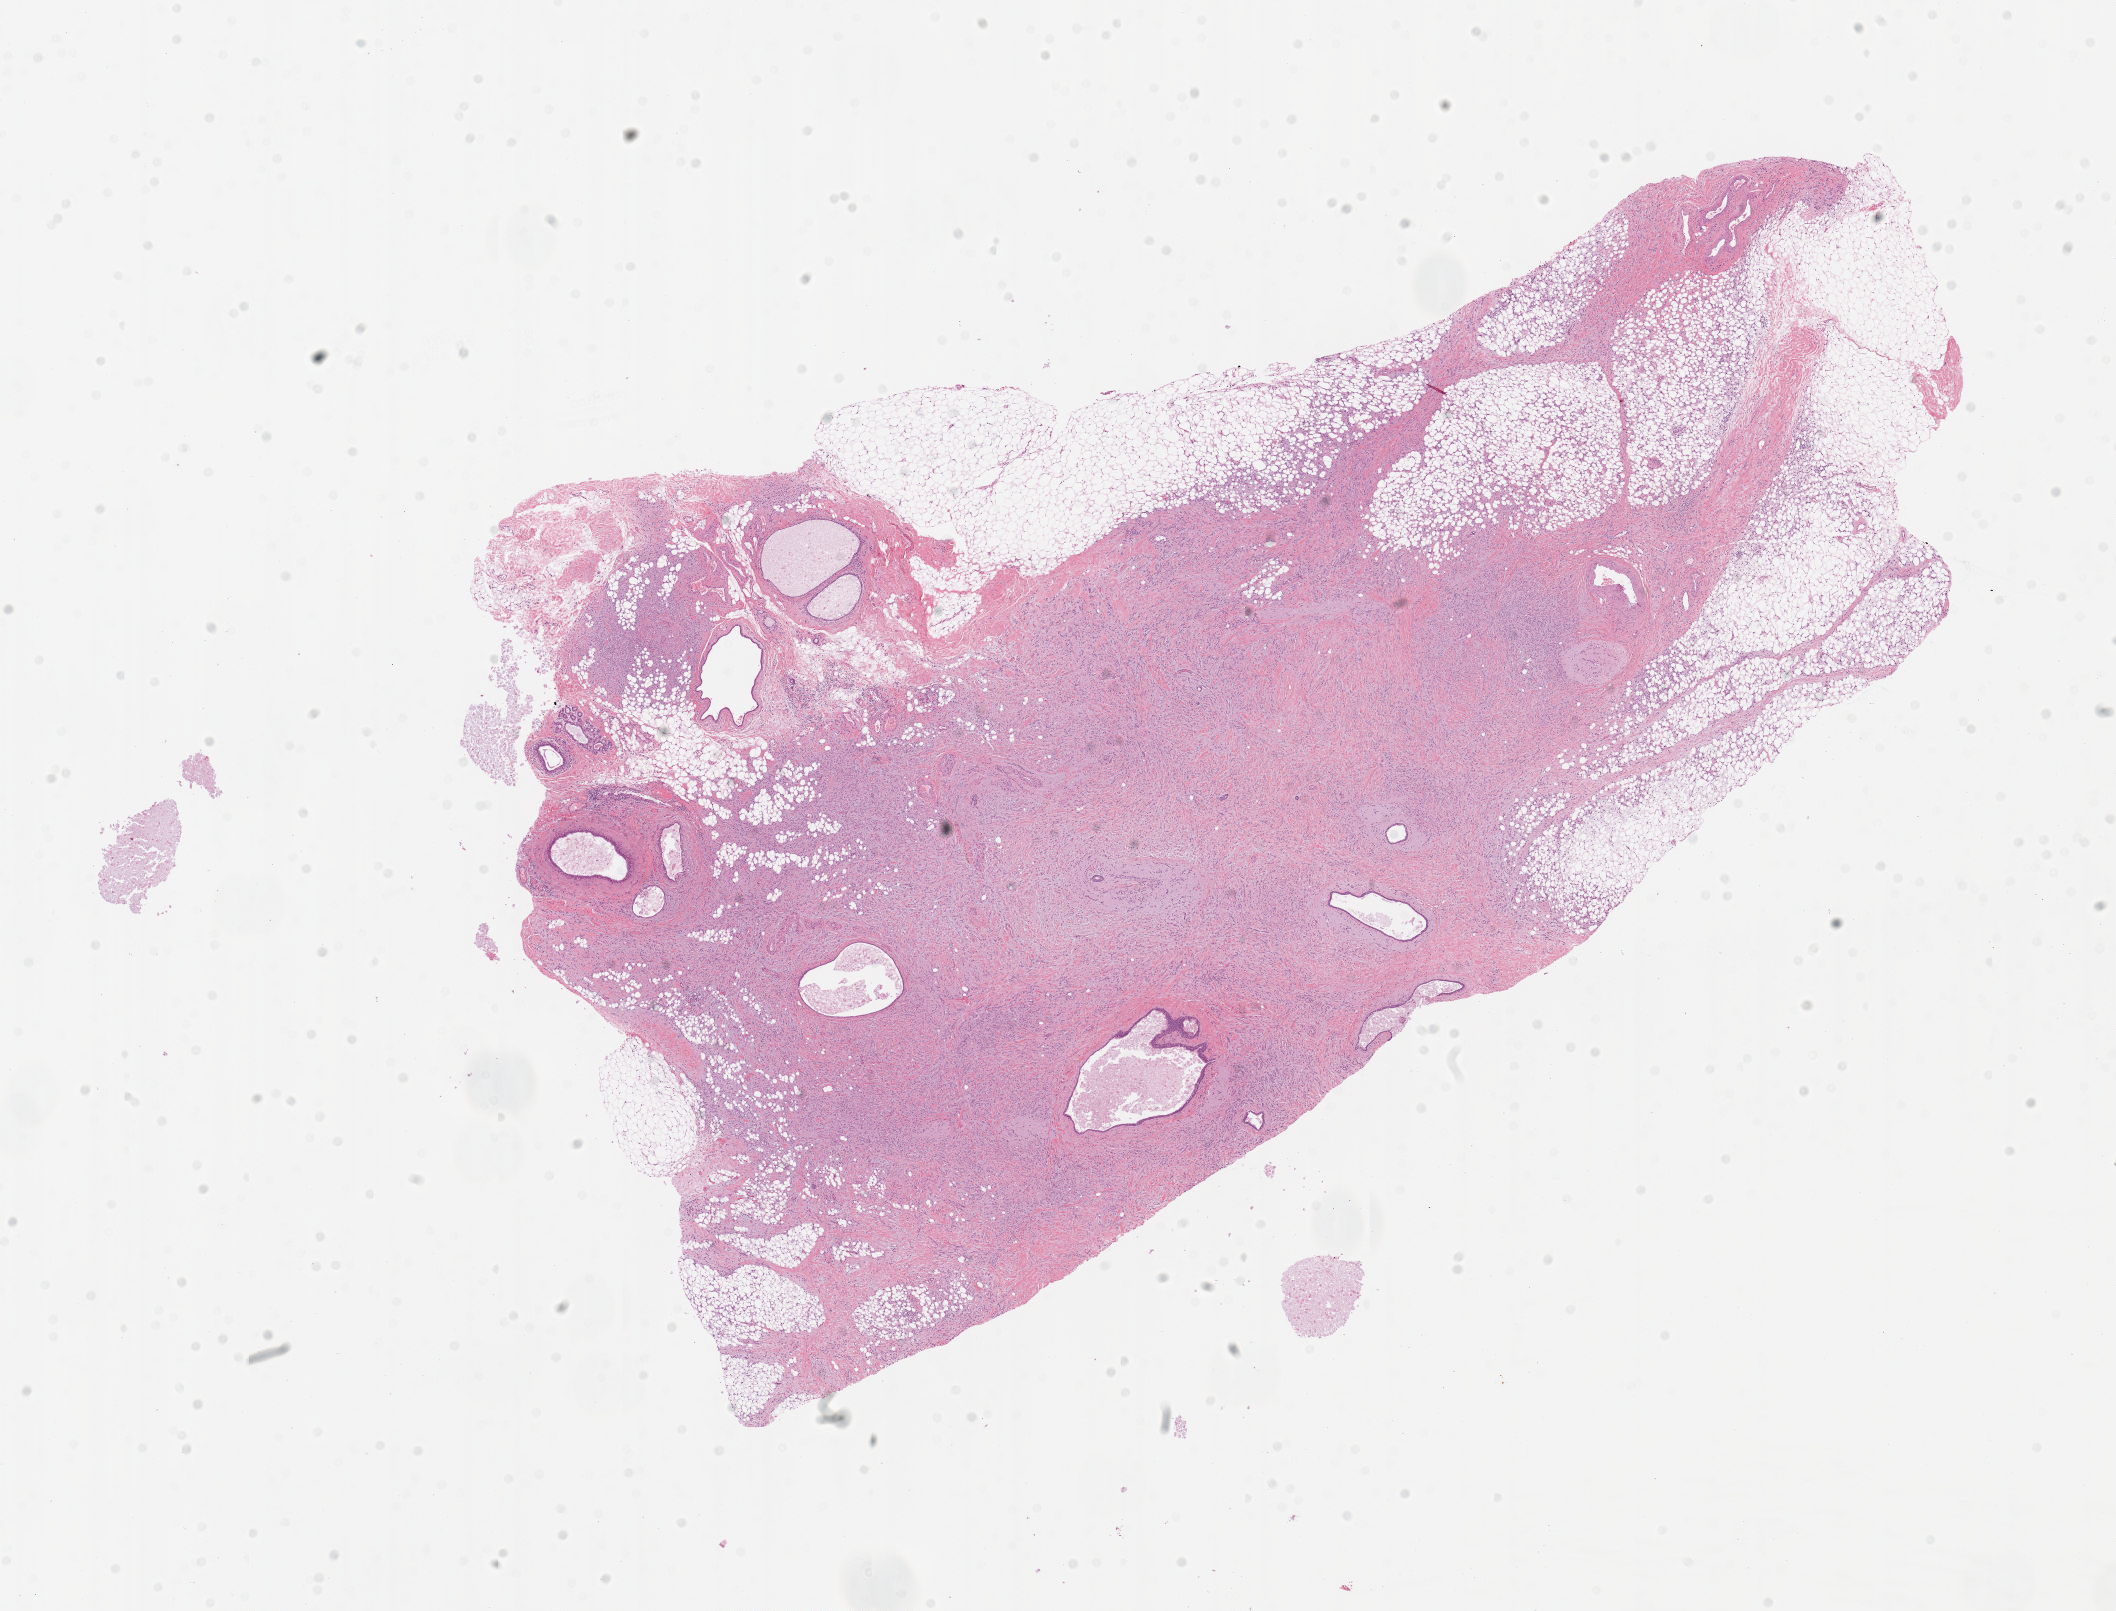
Digitized H&E tissue section (whole slide) — low-resolution overview of the scanned area, about 16.7 x 12.7 mm (acquisition: 20x scan); formalin-fixed paraffin-embedded (FFPE) diagnostic section; primary tumour sample from the breast. Patient sex: female.
AJCC pathologic stage: IIIA (7th edition). Lymph nodes positive (case pathology): 3 of 3 examined. Pathologic diagnosis: Lobular carcinoma, NOS.